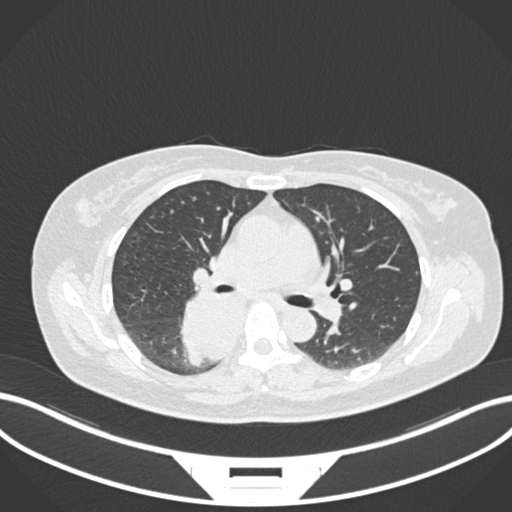
Chest CT, one axial slice; position 609 of 677 along the scan axis; reconstruction kernel B30f; 120 kVp; lung window (W 1500 / L -600 HU); 1 mm slice thickness; 512 × 512 image matrix, field of view 400 × 400 mm. Female patient, age 54 years. From the clinical record (not read from this slice): clinical TNM (as recorded): T4 N0 M0.
Outlined on this slice (rectangle marked by the reading radiologist):
- lung tumour (recorded histology: adenocarcinoma): bounding box [x1, y1, x2, y2] px = [180, 291, 253, 373]